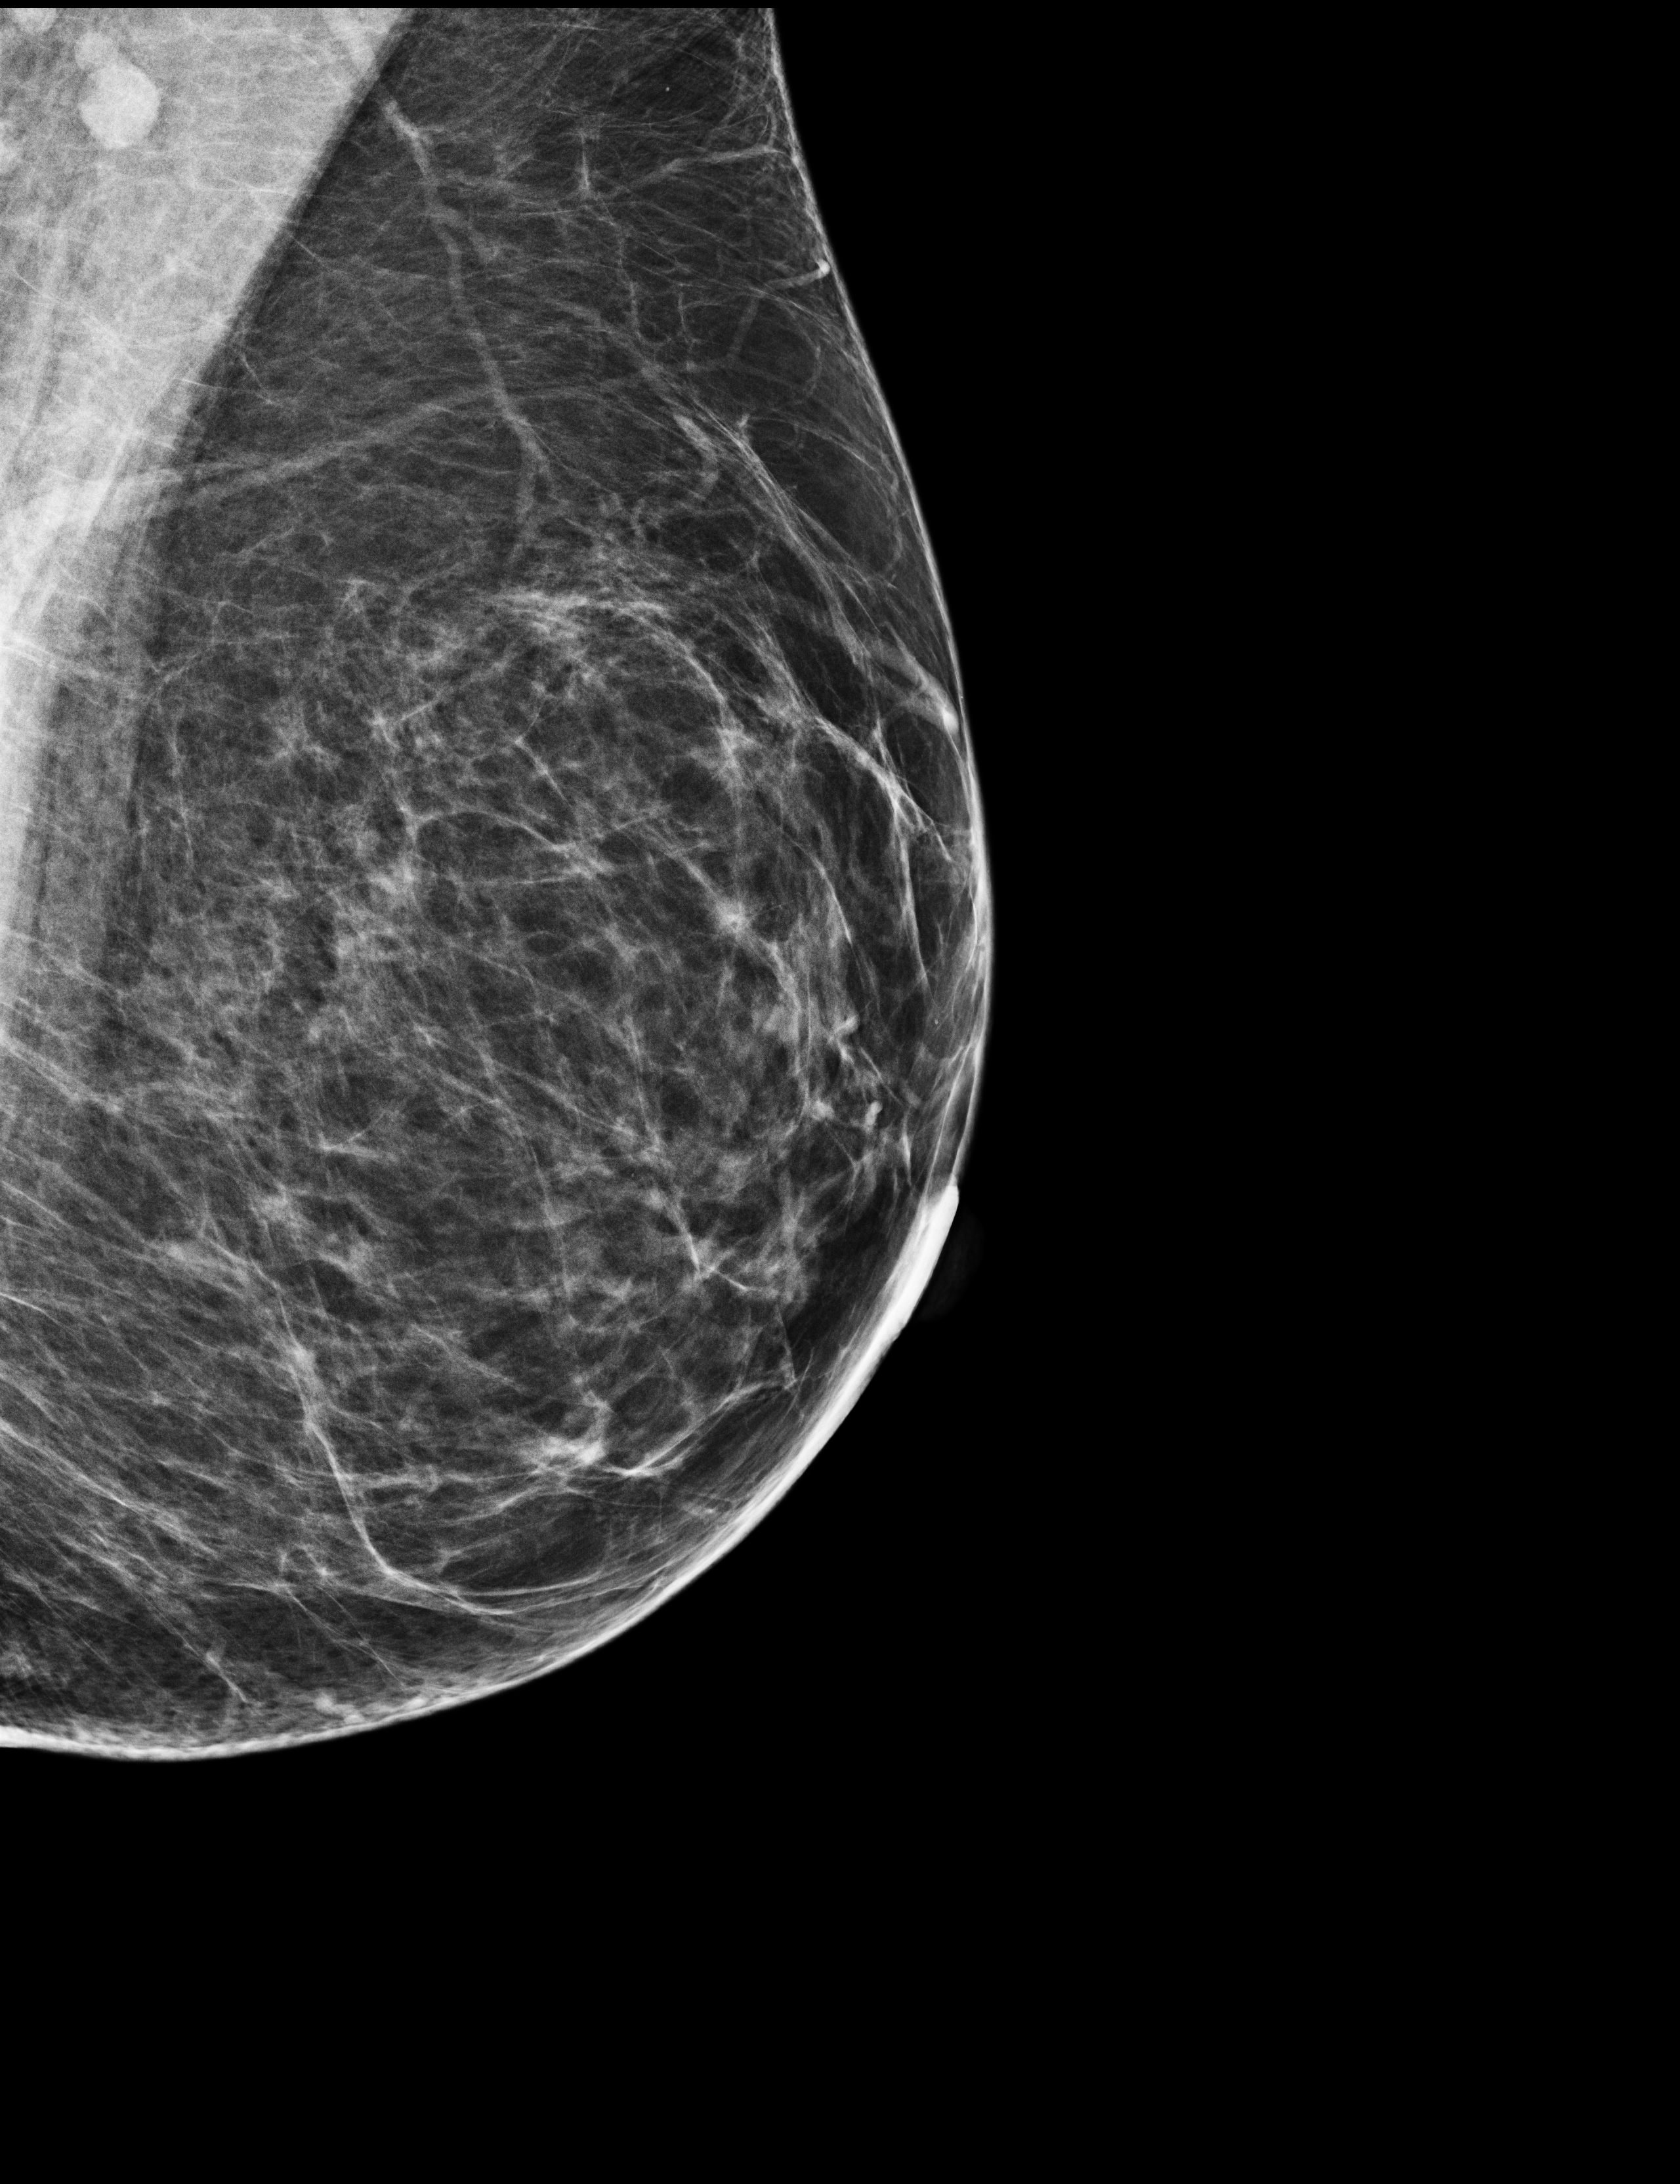
Annual screening mammography examination; compressed breast thickness 64 mm. Female patient, age 55 years.
Image type: full-field digital mammogram. Breast: left. Projection: mediolateral oblique (MLO) view.